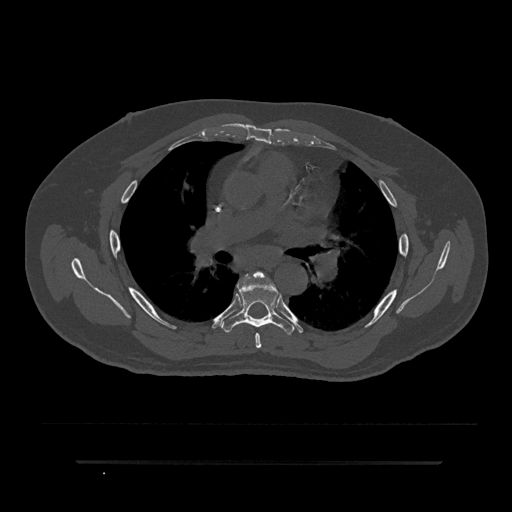
CT including the spine, one axial slice. Position 540 of 797 along the scan axis. Reconstruction kernel Br40s/3. Bone window (W 1800 / L 400 HU). 0.5 mm slice thickness. 512 × 512 image matrix, field of view 464 × 464 mm. Patient: male, 59 years. Case-level facts recorded for this patient, not image findings: primary cancer: bile ducts.
Annotated regions visible in this slice (semi-automatically segmented with operator editing):
- T5 vertebra: box from (x=253, y=272) to (x=264, y=348) px
- T6 vertebra: (x=221, y=280)–(x=294, y=335)